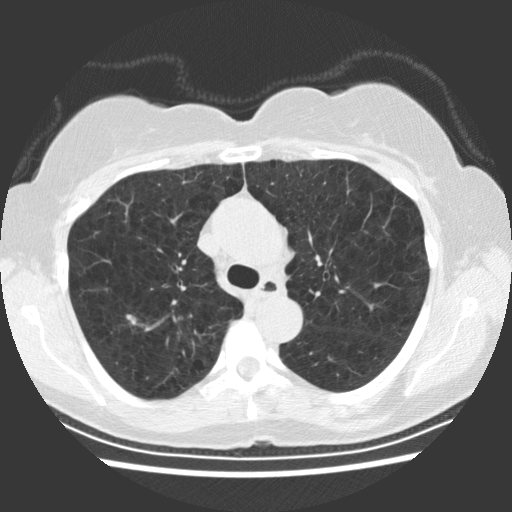
Chest CT (low-dose screening protocol), one axial image; first (baseline) screen; lung window (W 1500 / L -600 HU); 2.5 mm slice thickness; 120 kVp. Female, age 66 years at enrolment. Former smoker at enrolment.
- Expert reader's lesion annotation, bounding box <112,298,153,338> (left, top, right, bottom; pixels).
- Screening reader's record for this exam (one nodule recorded; not confirmed to be the boxed lesion): non-calcified nodule or mass ≥4 mm, right upper lobe, 10 × 8 mm, smooth margins, soft tissue attenuation.
- Official screen result: positive, change unspecified: nodule(s) >= 4 mm or enlarging nodule(s), mass(es), or other non-specific abnormalities suspicious for lung cancer.
- Later outcome: lung cancer diagnosed 54 days after this screen — squamous cell carcinoma, keratinizing, NOS, right upper lobe, poorly differentiated (G3), stage IA (AJCC 6th edition), 11 mm at pathology.